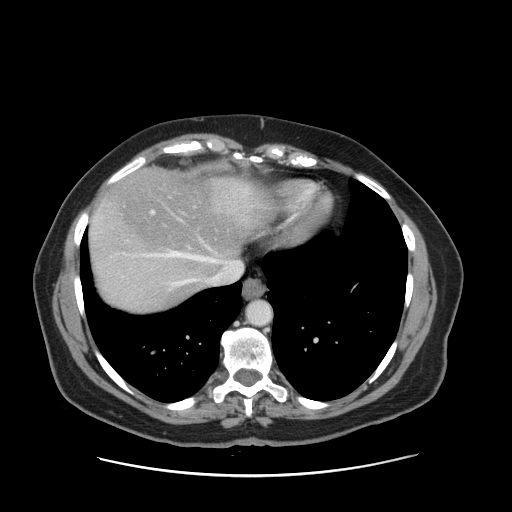
Contrast-enhanced abdominal CT, one axial slice; slice 134 of 161 in the series (ordered by position); intravenous contrast given; soft-tissue window (W 400 / L 40 HU); 2.5 mm slice thickness; 512 × 512 image matrix. Female patient, age 62 years. Case-level facts recorded for this patient, not image findings: diagnosis: colorectal cancer liver metastases, imaged before liver resection; multiple liver metastases: no; largest metastasis: 2.5 cm; disease in both lobes: no.
Outlined on this slice (manually delineated by an expert):
- hepatic veins: bounding box <124,188,242,288> (left, top, right, bottom; pixels)
- liver: <90,169,270,312>
- planned liver remnant (the part of the liver to remain after resection): <95,169,271,277>
- portal vein (with intrahepatic branches): <151,196,185,214>